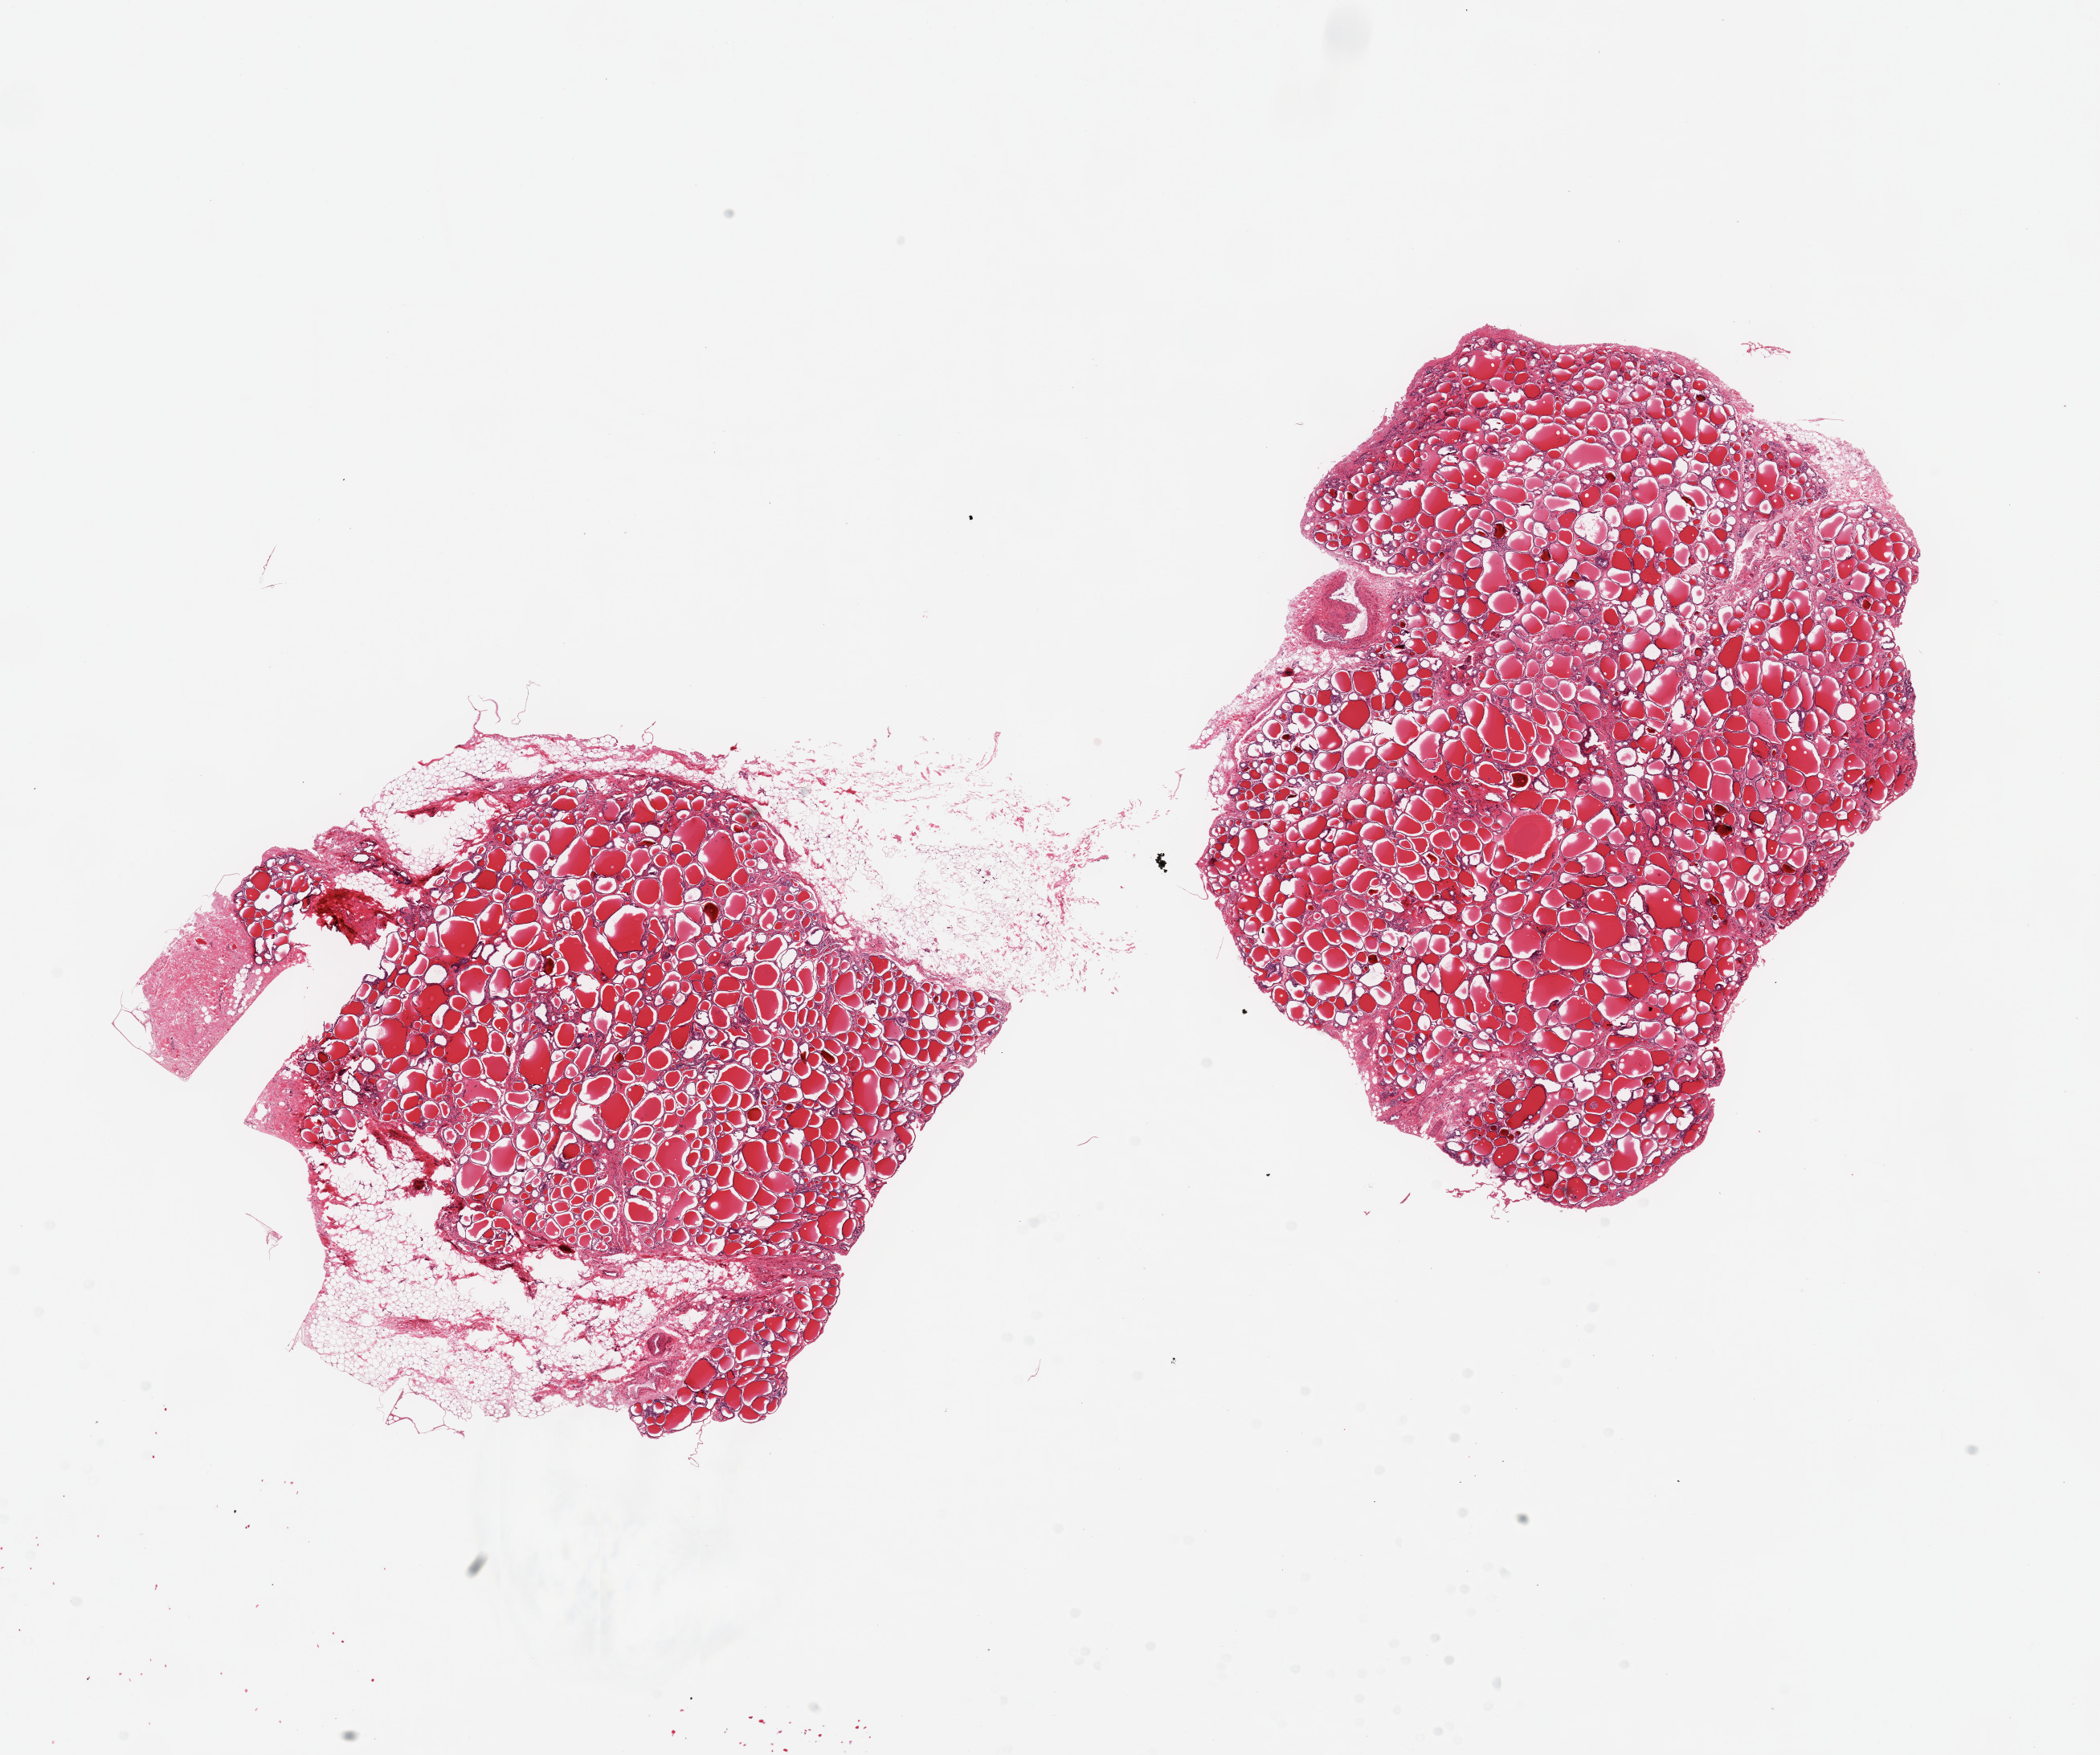
Haematoxylin and eosin whole-slide image, low-resolution overview of the scanned area, about 20.7 x 17.3 mm (slide scanned at 20x), PAXgene-fixed paraffin-embedded (PFPE) section, target tissue: thyroid, tissue donor sample. Male donor.
Pathologist's review note for this sample: 2 pieces; one piece includes ~30% fat and connective tissue, attached portion of large vessel in second piece.